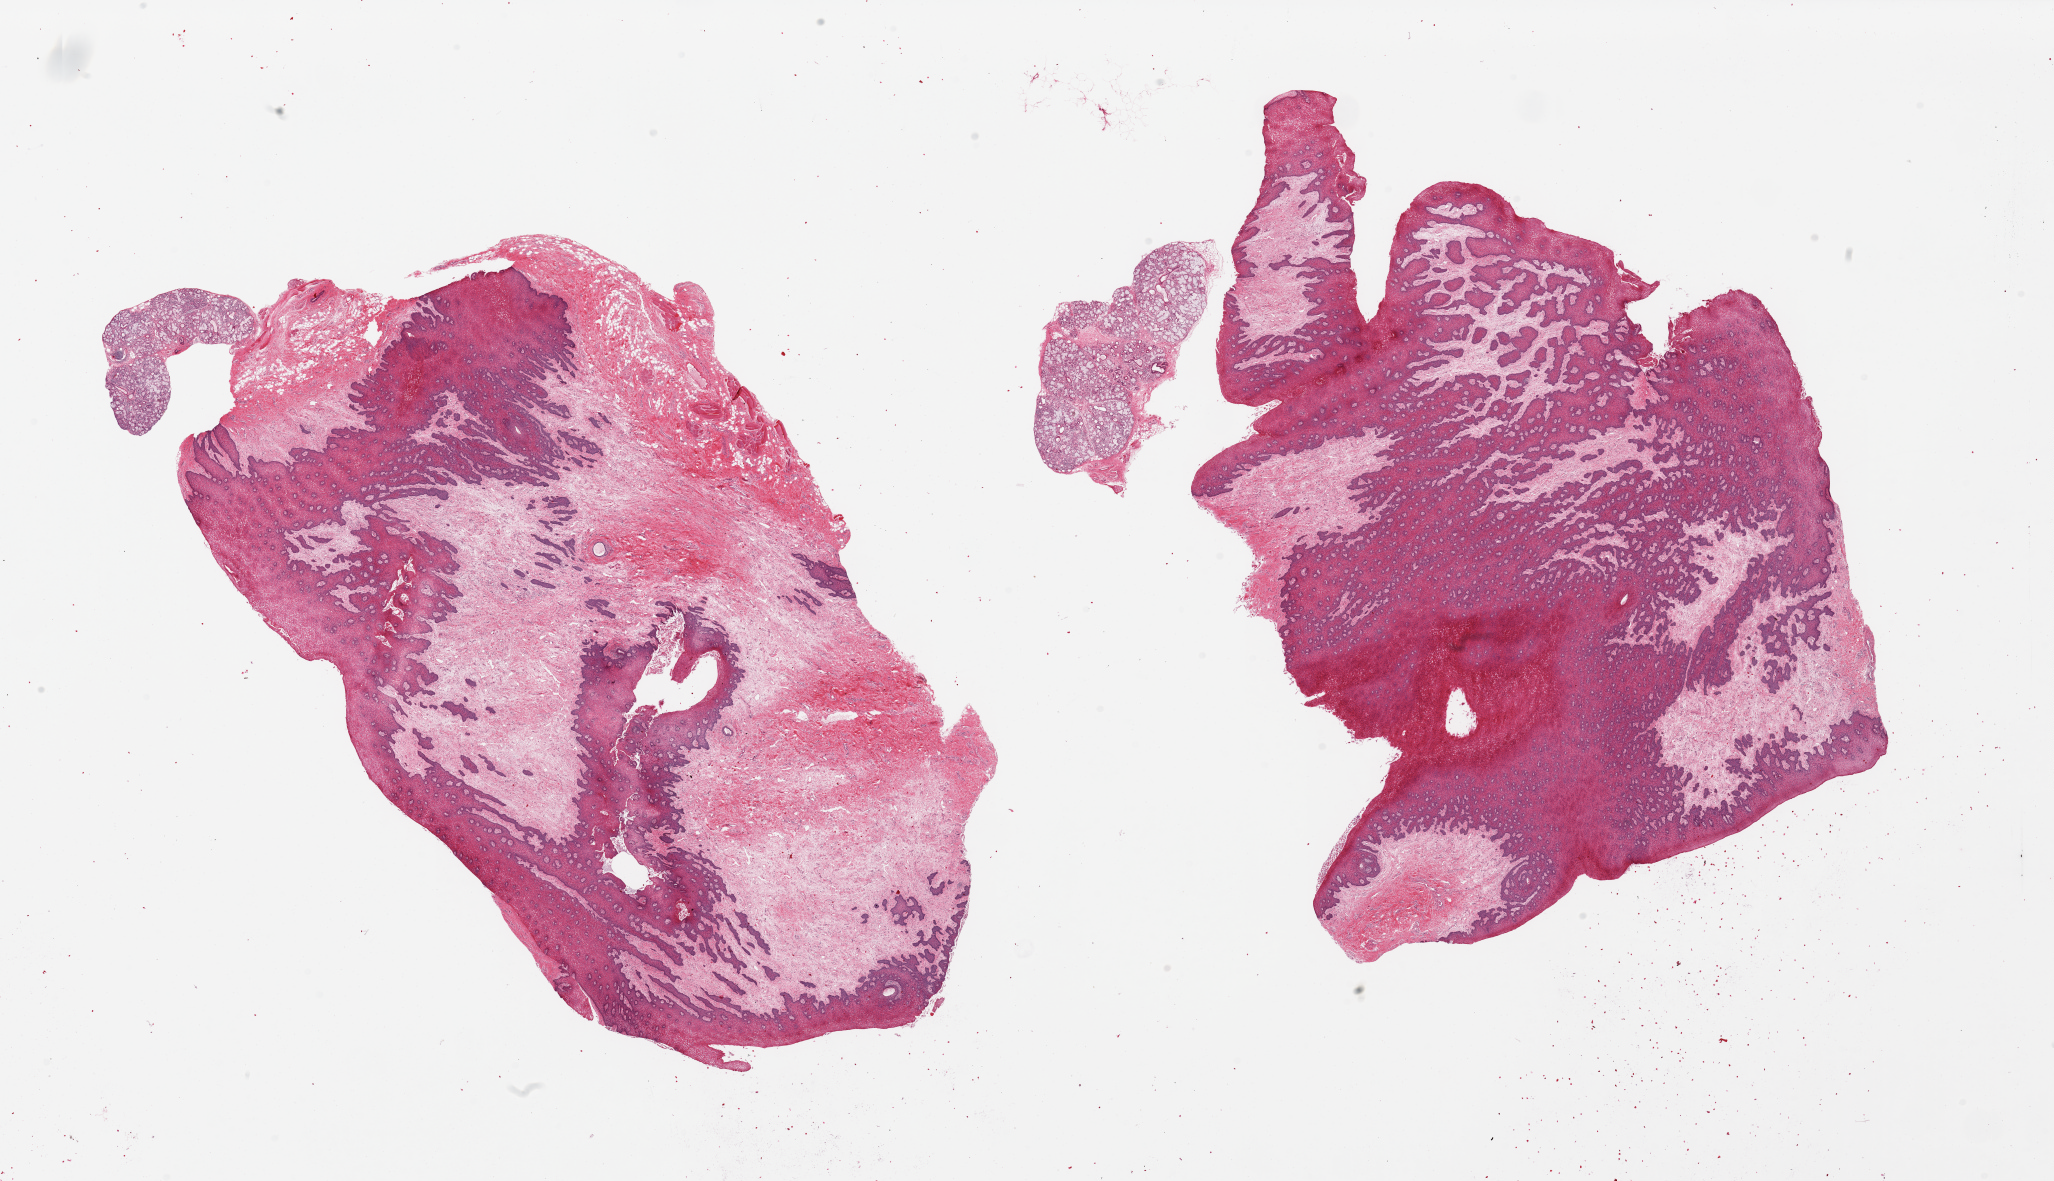
Digitized haematoxylin and eosin-stained section — whole scanned area (about 32.5 x 18.7 mm, from a 20x scan) shown as a low-resolution overview, PAXgene-fixed, paraffin-embedded tissue, section of minor salivary gland (target tissue), donor tissue sample. Donor: male.
Reviewer comment on this tissue sample: 2 pieces, chronically inflamed salivary gland comprises only ~5% of total tissue, rest is predominantly mucosa and stroma.